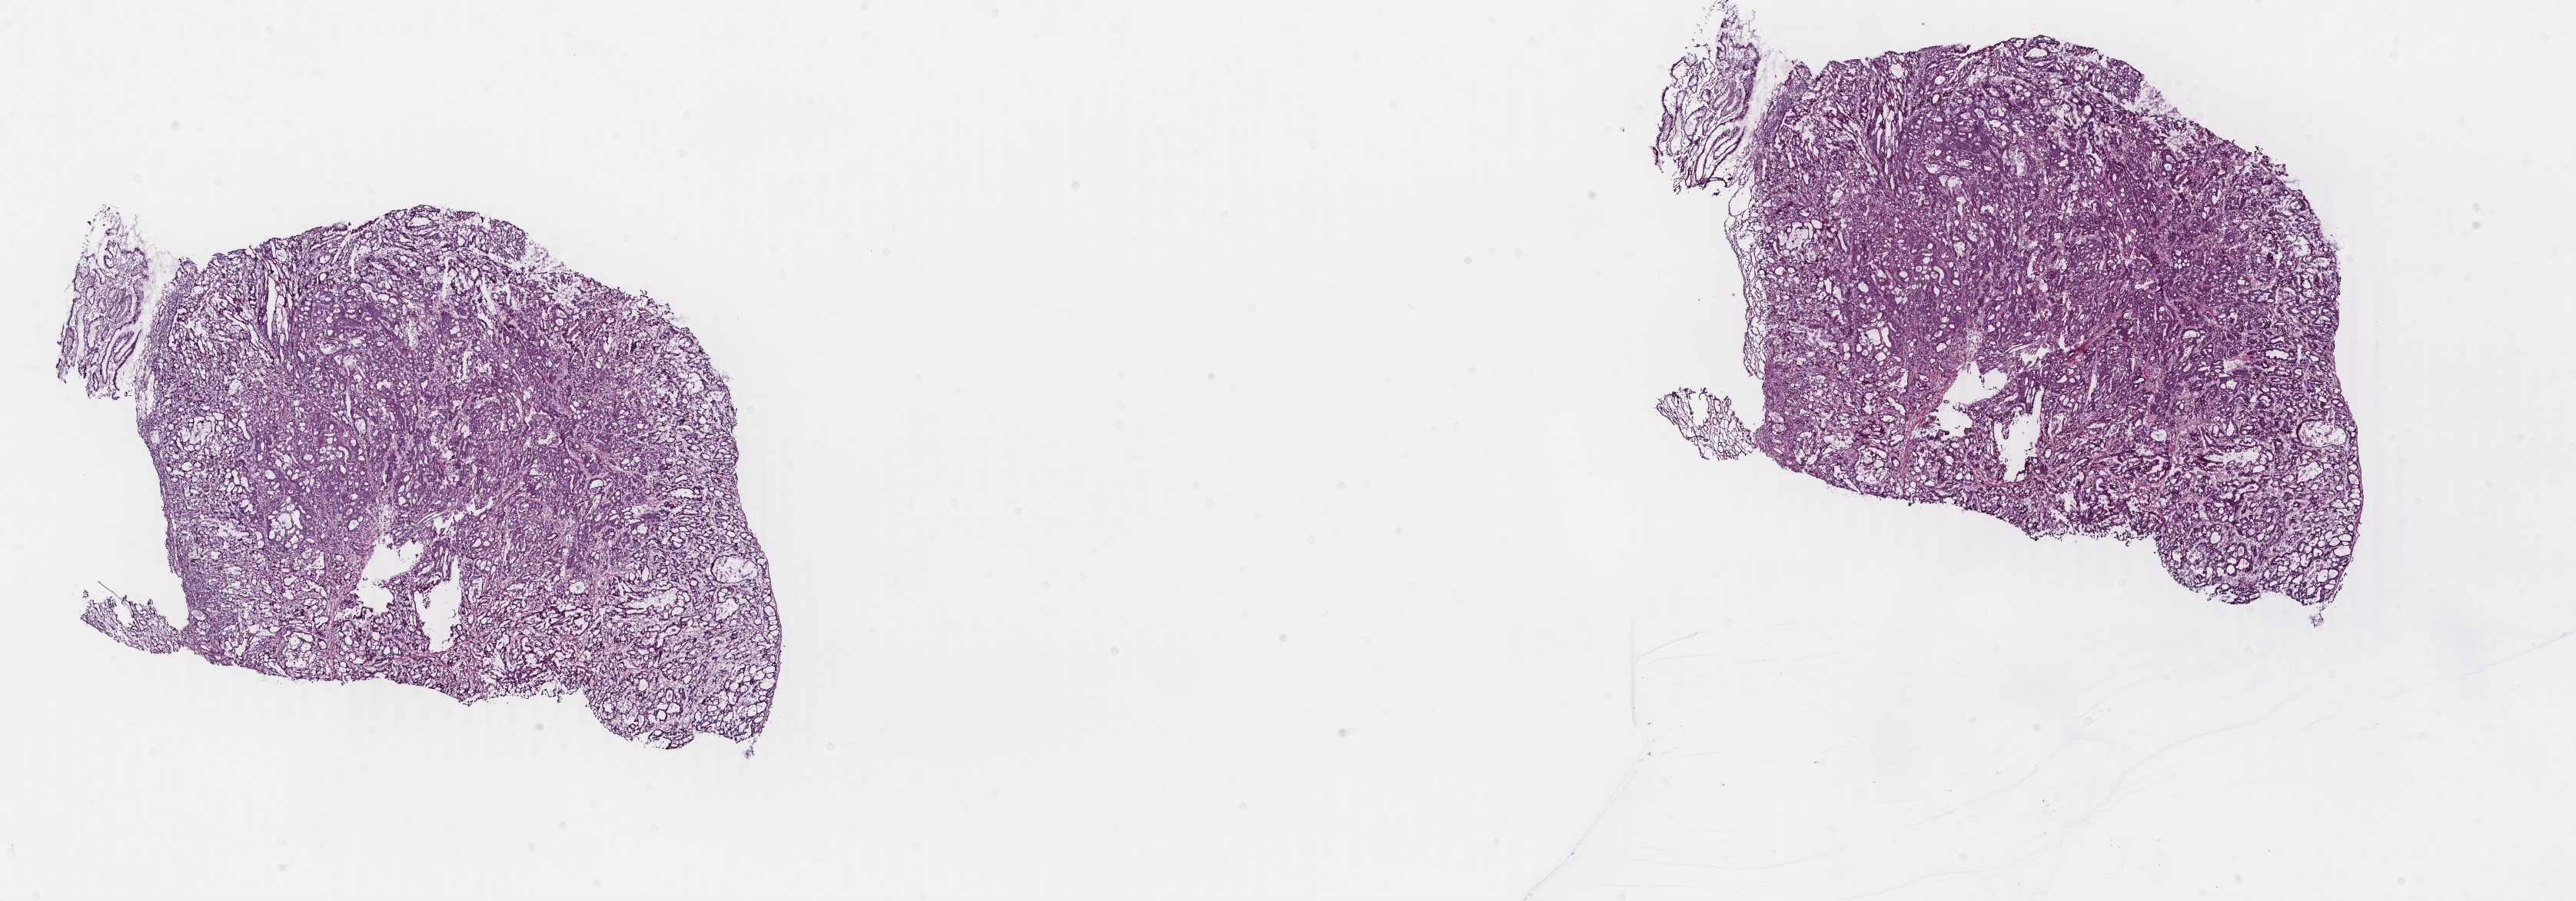
Digitized H&E-stained tissue section (whole slide), a low-resolution overview of the entire scanned area, about 26.7 x 9.3 mm (acquisition: 40x scan), frozen section from the top of the tissue portion, sample: primary tumour, stomach. Patient: female, age at initial diagnosis 75 years. Histologic grade: G3 (poorly differentiated). Composition of this section per pathologist review: tumour cells 90%, tumour nuclei 90%, normal cells 0%, stromal cells 10%, necrosis 0%. Infiltration values recorded for this section: lymphocyte infiltration 20%, monocyte infiltration 20%, neutrophil infiltration 20%.
AJCC pathologic stage: IIIC. TNM: T4a N3a M0. Pathologic diagnosis: Mucinous adenocarcinoma (gastric antrum). Lymph nodes positive (case pathology): 11 of 26 examined.